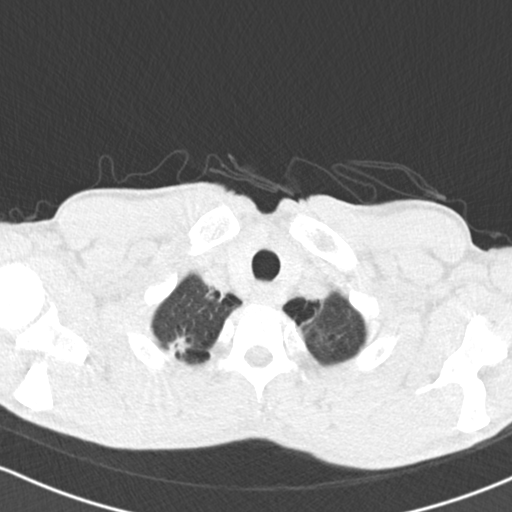
Low-dose screening chest CT, one axial slice. Reconstruction kernel B30f. Lung window (W 1500 / L -600 HU). 2 mm slice thickness. 512 × 512 image matrix, field of view 312 × 312 mm.
Annotated regions visible in this slice (expert manual segmentation):
- lesion 1 (tumor, upper lobe of right lung): bounding box [x1, y1, x2, y2] px = [168, 336, 189, 357]